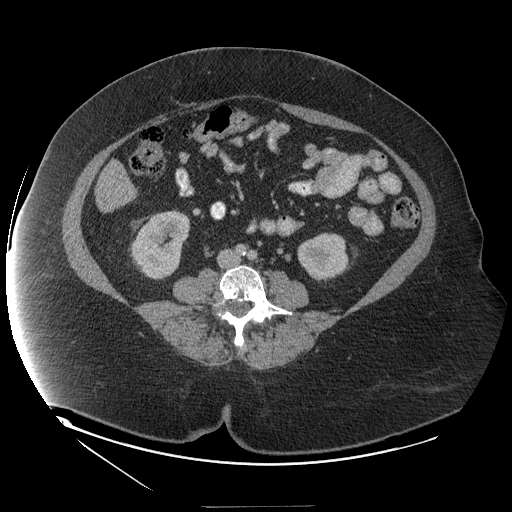
Contrast-enhanced abdominal CT (liver protocol), one axial slice. Position 23 of 127 along the scan axis. Reconstruction kernel STANDARD. 140 kVp. Soft-tissue window (W 400 / L 40 HU). 2.5 mm slice thickness. 512 × 512 image matrix. From the clinical record (not read from this slice): diagnosis: hepatocellular carcinoma (patient treated with transarterial chemoembolisation; whether this scan precedes or follows treatment is not stated here); TNM stage (as recorded): Stage-II; Child-Pugh class: A; tumour nodularity: multinodular.
Outlined on this slice (semi-automatic segmentation, software-assisted and operator-edited):
- liver parenchyma outside the tumour (the mass and vessels are separate outlines, so this box may not span the whole liver): box from (x=96, y=160) to (x=130, y=212) px